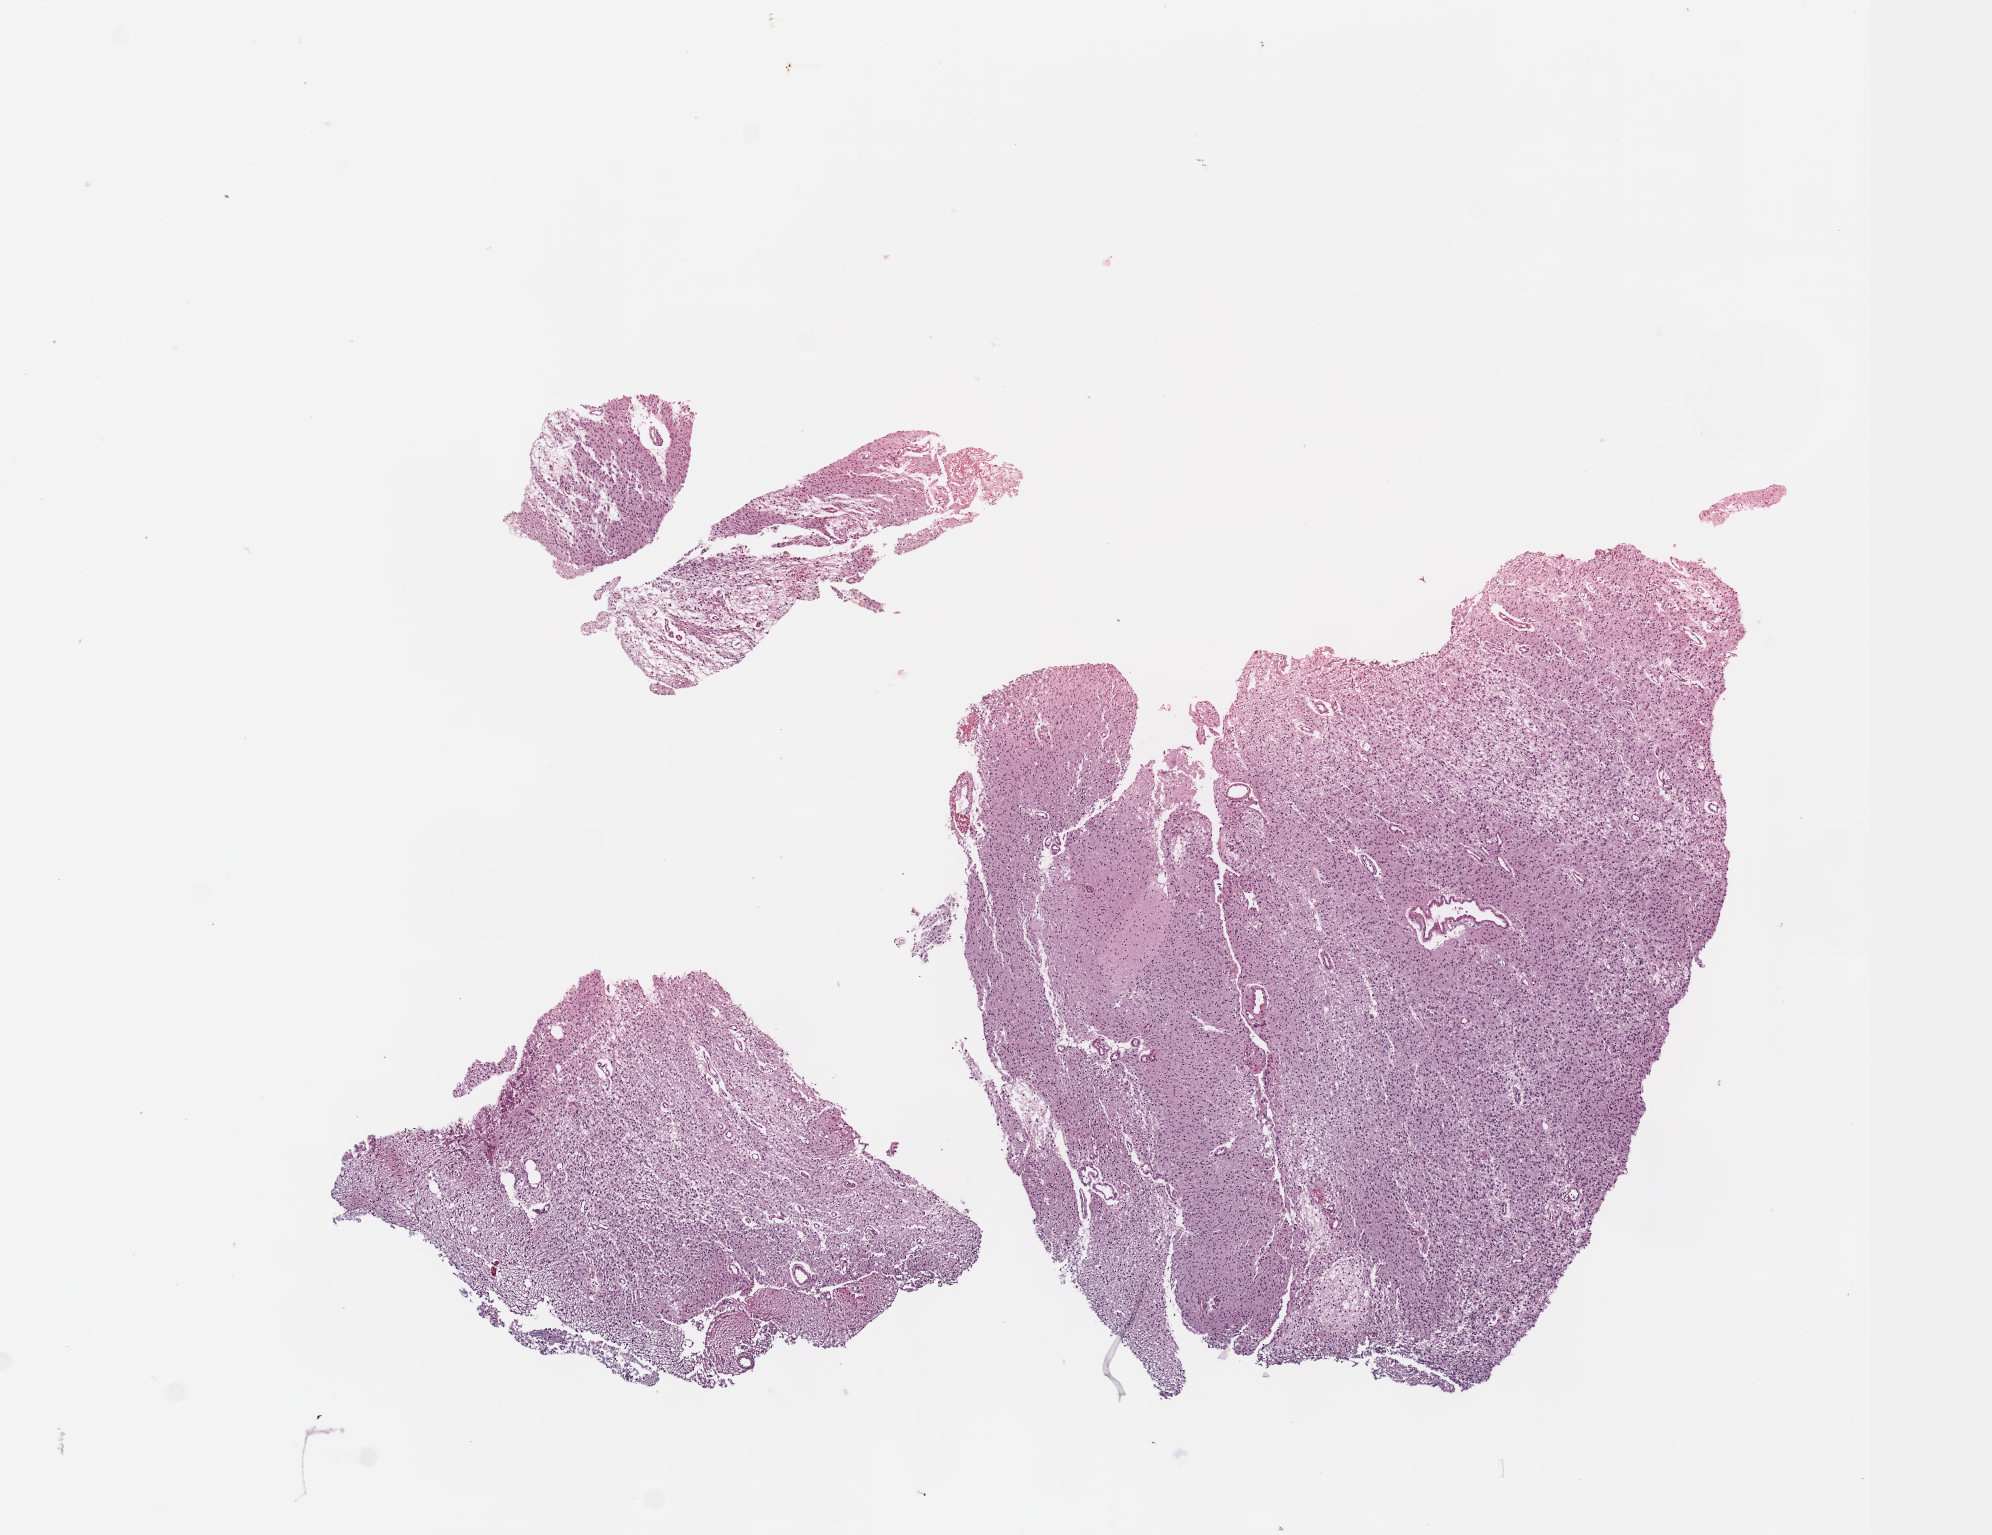
Digitized H&E tissue section (whole slide), a low-resolution overview of the entire scanned area, about 8.0 x 6.2 mm (slide scanned at 40x); FFPE section; sample: primary tumour, brain. Male, age 25 years at initial diagnosis. Histologic grade: G2 (moderately differentiated).
Diagnosis: Mixed glioma (cerebrum). Laterality: right.